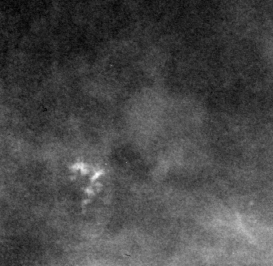
Cropped region of a digitized screen-film mammogram centred on a radiologist-marked abnormality; right breast; CC view.
- Marked abnormality: calcifications, morphology pleomorphic, distribution clustered; BI-RADS assessment category 2; benign; no additional work-up was recommended (benign without callback).